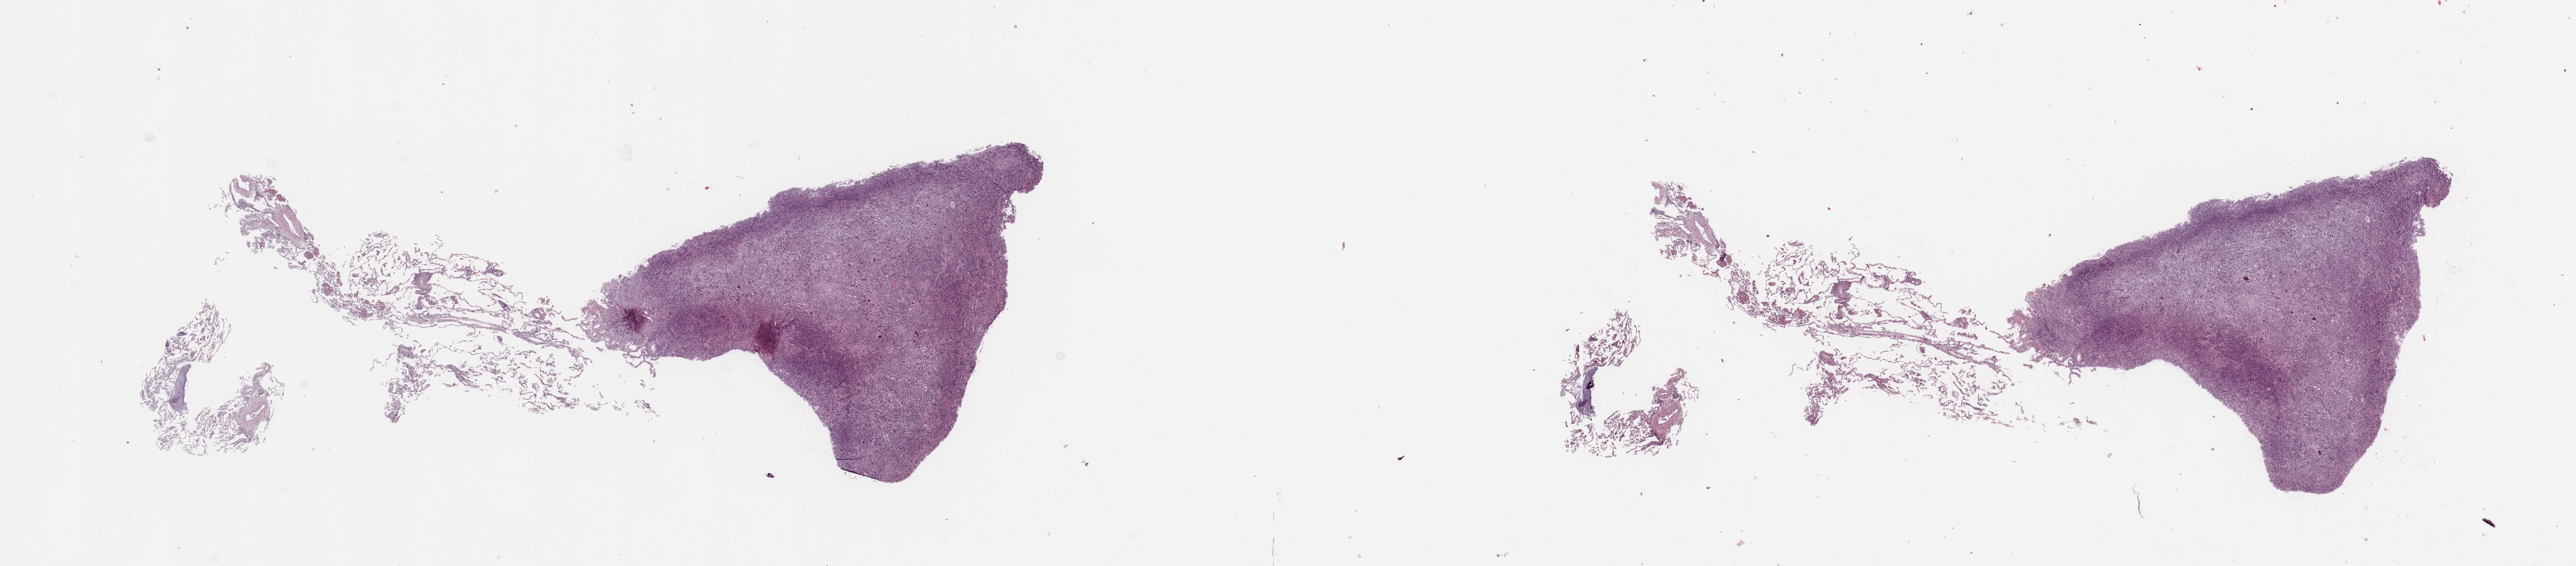
Whole-slide histology image, Hematoxylin and eosin (H&E) stained, low-resolution overview of the scanned area, about 28.5 x 6.3 mm (slide scanned at 20x); tumour tissue sample, sampled site: lung. Male, 64 y/o. Histologic grade: G3 (poorly differentiated). Pathologist review of this section (percent, as recorded): tumour nuclei 80%, necrosis 5%.
Diagnosis: Adenocarcinoma, NOS. AJCC pathologic stage: IA1.